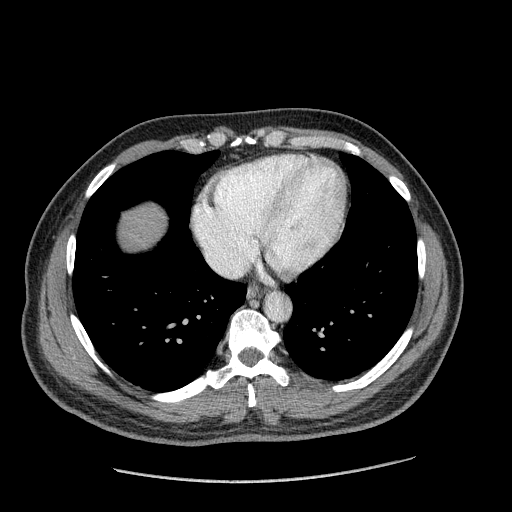
Contrast-enhanced abdominal CT (liver protocol), one axial slice. Position 175 of 182 along the scan axis. 120 kVp. Soft-tissue window (W 400 / L 40 HU). 2.5 mm slice thickness. 512 × 512 image matrix, field of view 400 × 400 mm. Case-level facts recorded for this patient, not image findings: diagnosis: hepatocellular carcinoma (patient treated with transarterial chemoembolisation; whether this scan precedes or follows treatment is not stated here); TNM stage (as recorded): Stage-I; Child-Pugh class: A.
Outlined on this slice (semi-automatic segmentation, software-assisted and operator-edited):
- abdominal aorta: bounding box <264,293,291,321> (left, top, right, bottom; pixels)
- liver parenchyma outside the tumour (the mass and vessels are separate outlines, so this box may not span the whole liver): <122,206,164,248>